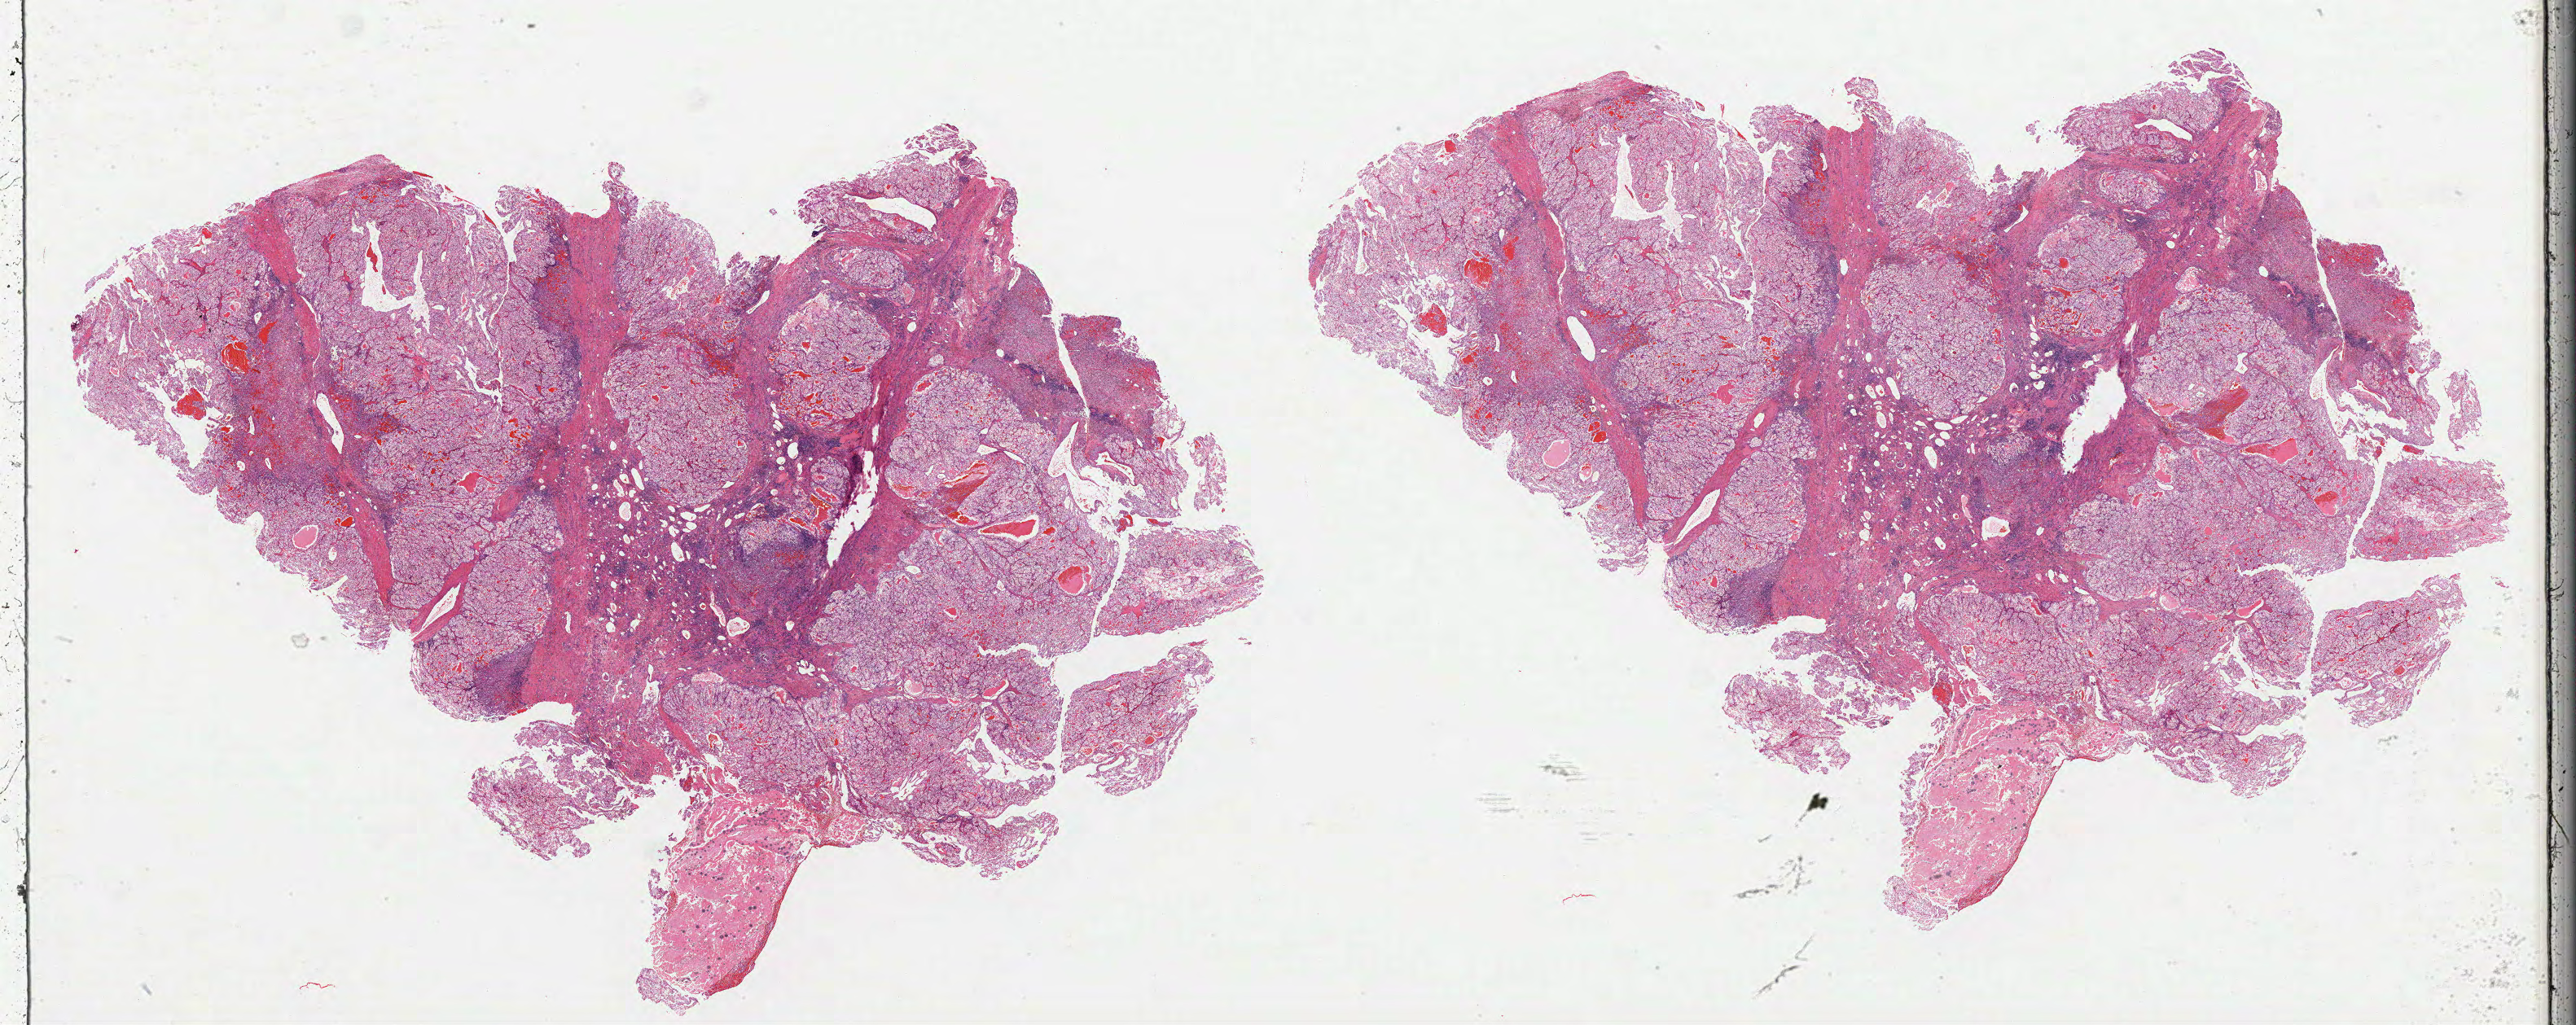
Hematoxylin and eosin (H&E) stained whole-slide image, whole scanned area (about 51.0 x 20.3 mm) shown as a low-resolution overview. Formalin-fixed paraffin-embedded (FFPE) diagnostic section. Kidney, primary tumour sample. Patient: male, age at initial diagnosis 67 years. Histologic grade: G2 (moderately differentiated).
* AJCC pathologic stage: III (6th edition)
* diagnosis: Clear cell adenocarcinoma, NOS